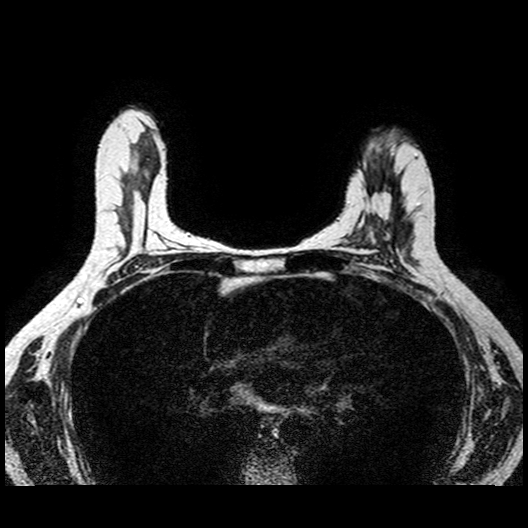
Breast MRI examination; 2 images, each one mid-volume slice chosen by position. Age decade 40s.
Image 1: fluid-sensitive (T2/STIR) axial slice, series "T2W_TSE SENSE", slice 41 of 81, 2 mm slice thickness.
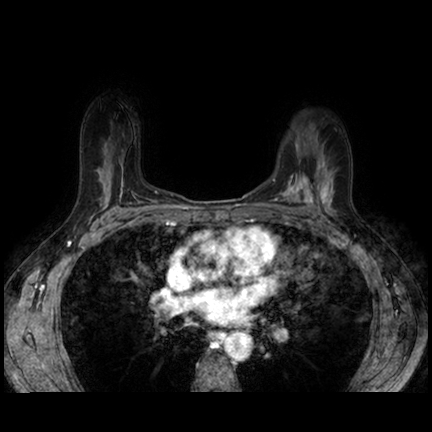
Image 2: axial dynamic contrast-enhanced T1-weighted image, series "AX BLISS_AUTO SENSE", slice 41 of 81, dynamic phase 6 of 10, 4 mm slice thickness.
Pathology recorded for this patient (not read from these images): pathology diagnosis: intraductal CA (left breast); receptor status (as recorded): ER neg, PR neg, HER2 pos; Ki-67 (as recorded): high prolif.